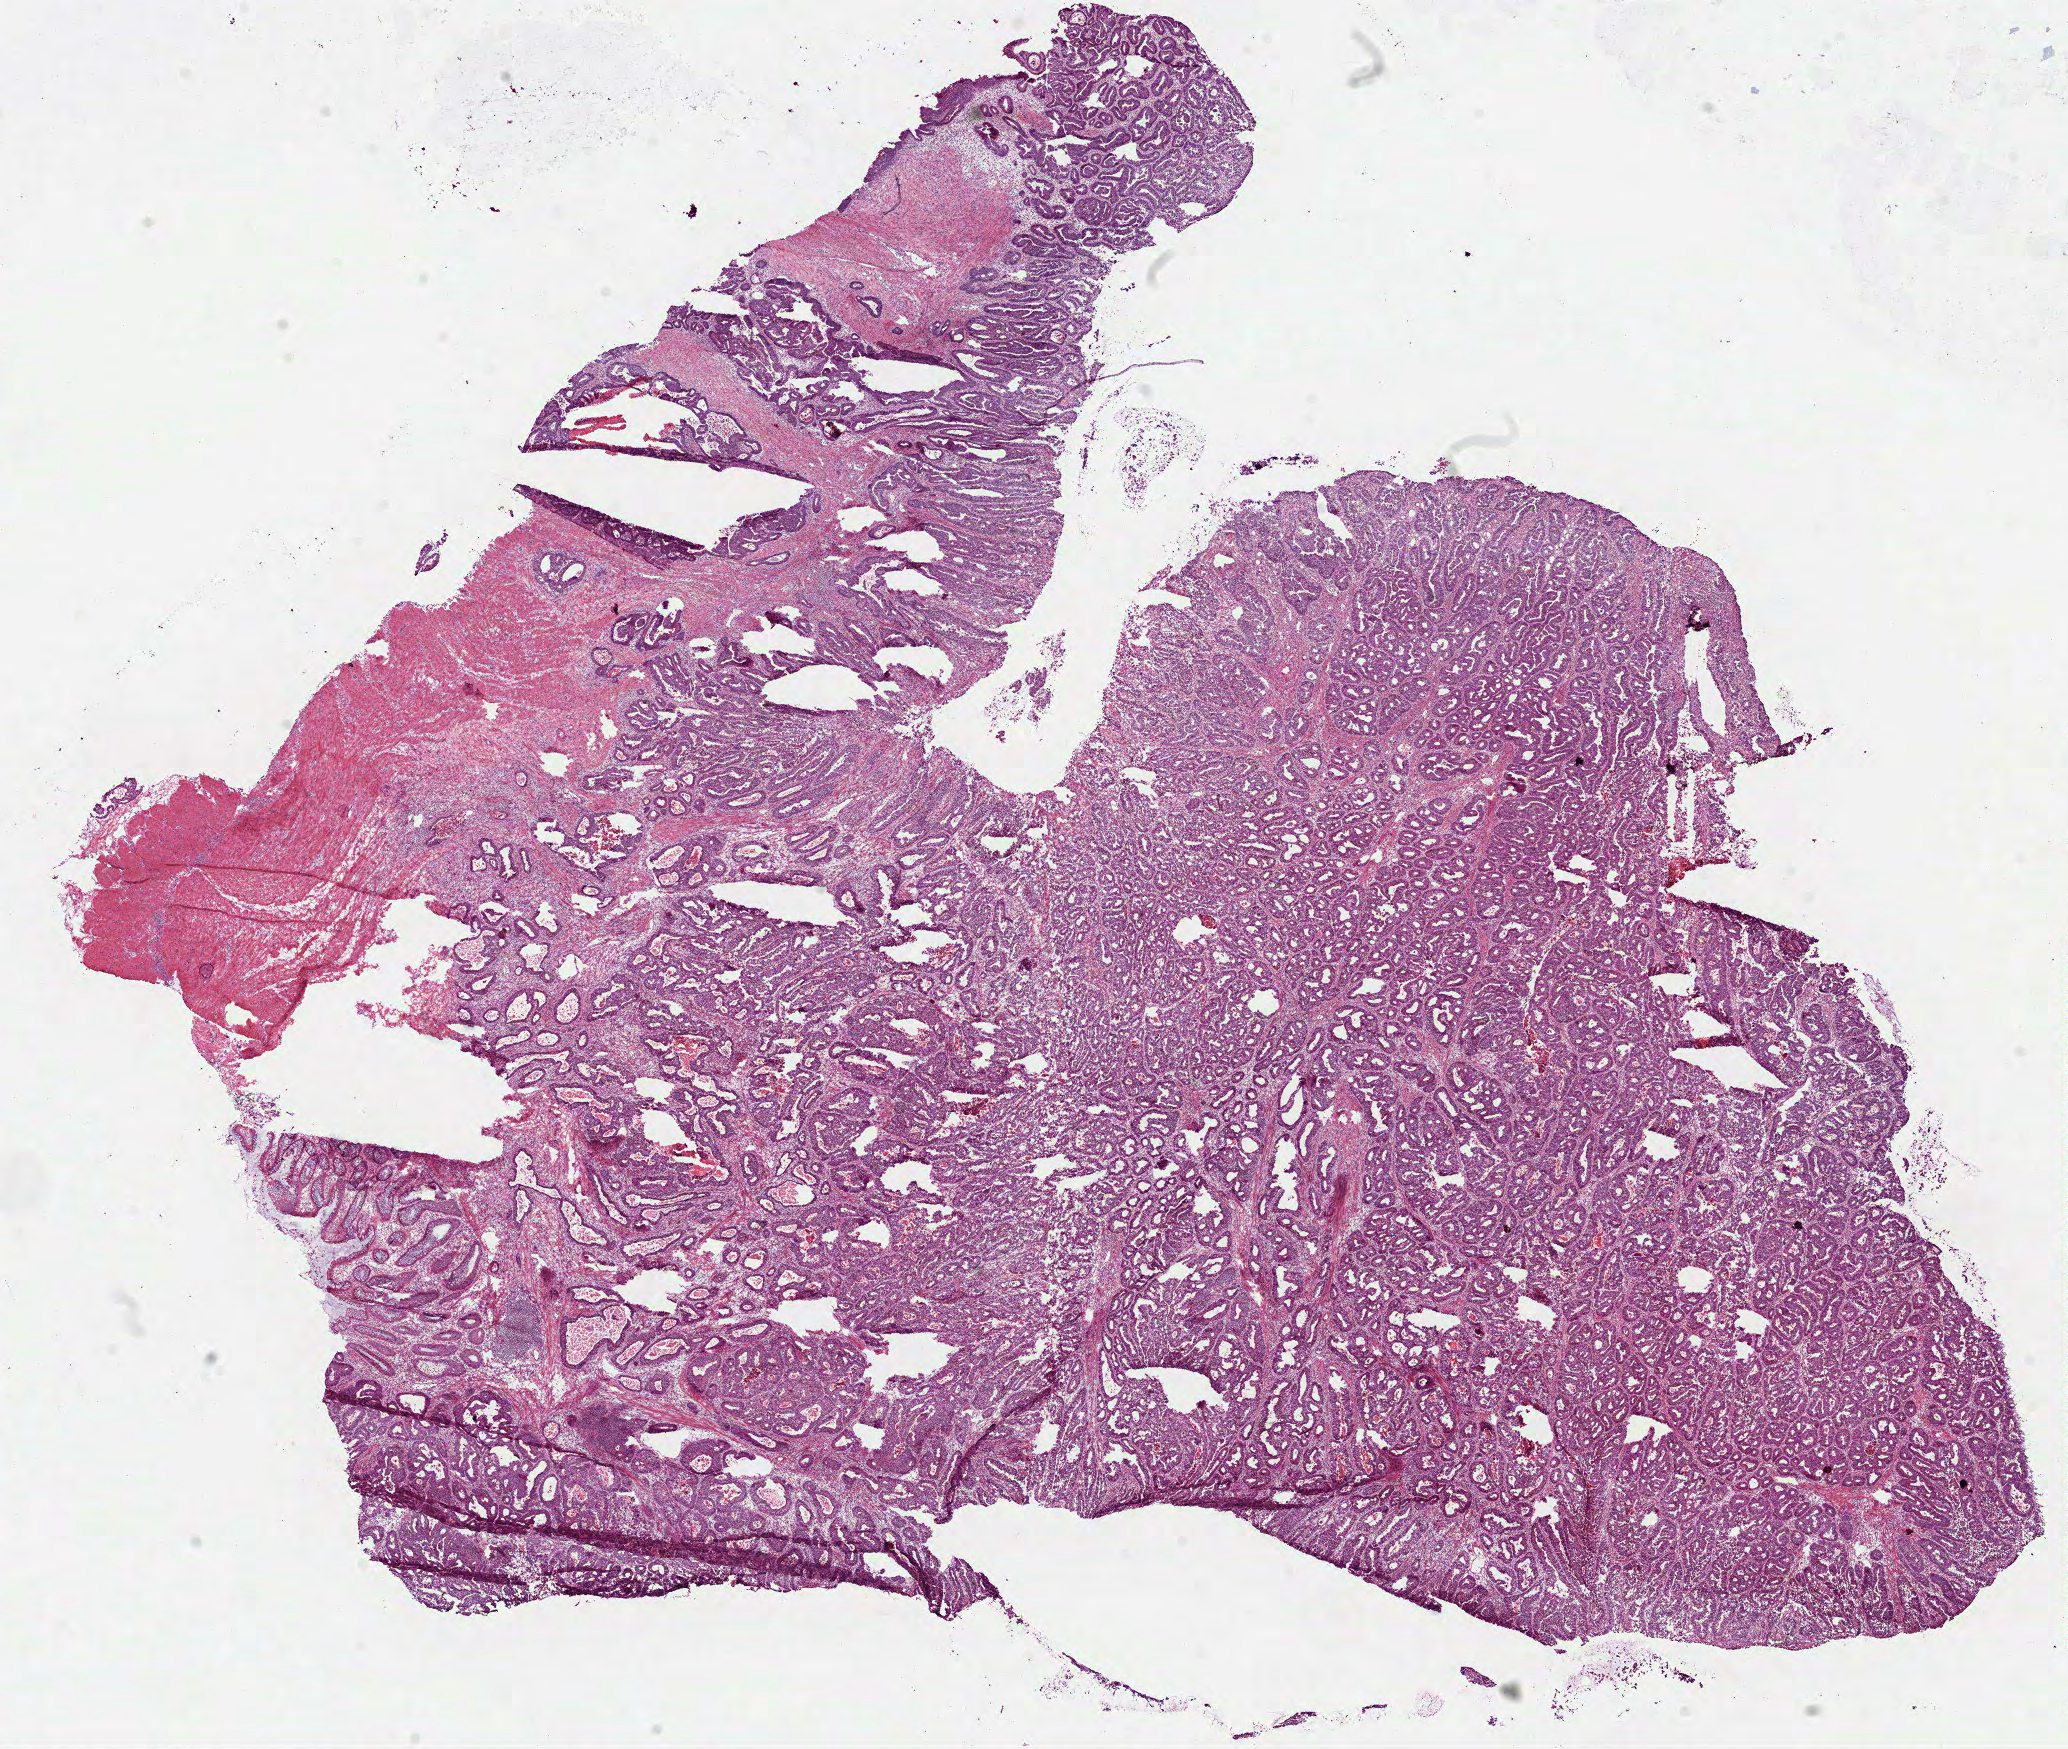
Hematoxylin and eosin (H&E) stained whole-slide image, whole scanned area (about 16.7 x 14.1 mm) shown as a low-resolution overview, frozen section, sample: primary tumour, colon. Patient: female, age at initial diagnosis 77 years. Pathologist review of this section (percent, as recorded): tumour cells 80%, tumour nuclei 80%, normal cells 5%, stromal cells 10%, necrosis 5%.
Lymph nodes positive (case pathology): 0 of 3 examined. Histologic diagnosis: Adenocarcinoma, NOS (sigmoid colon).